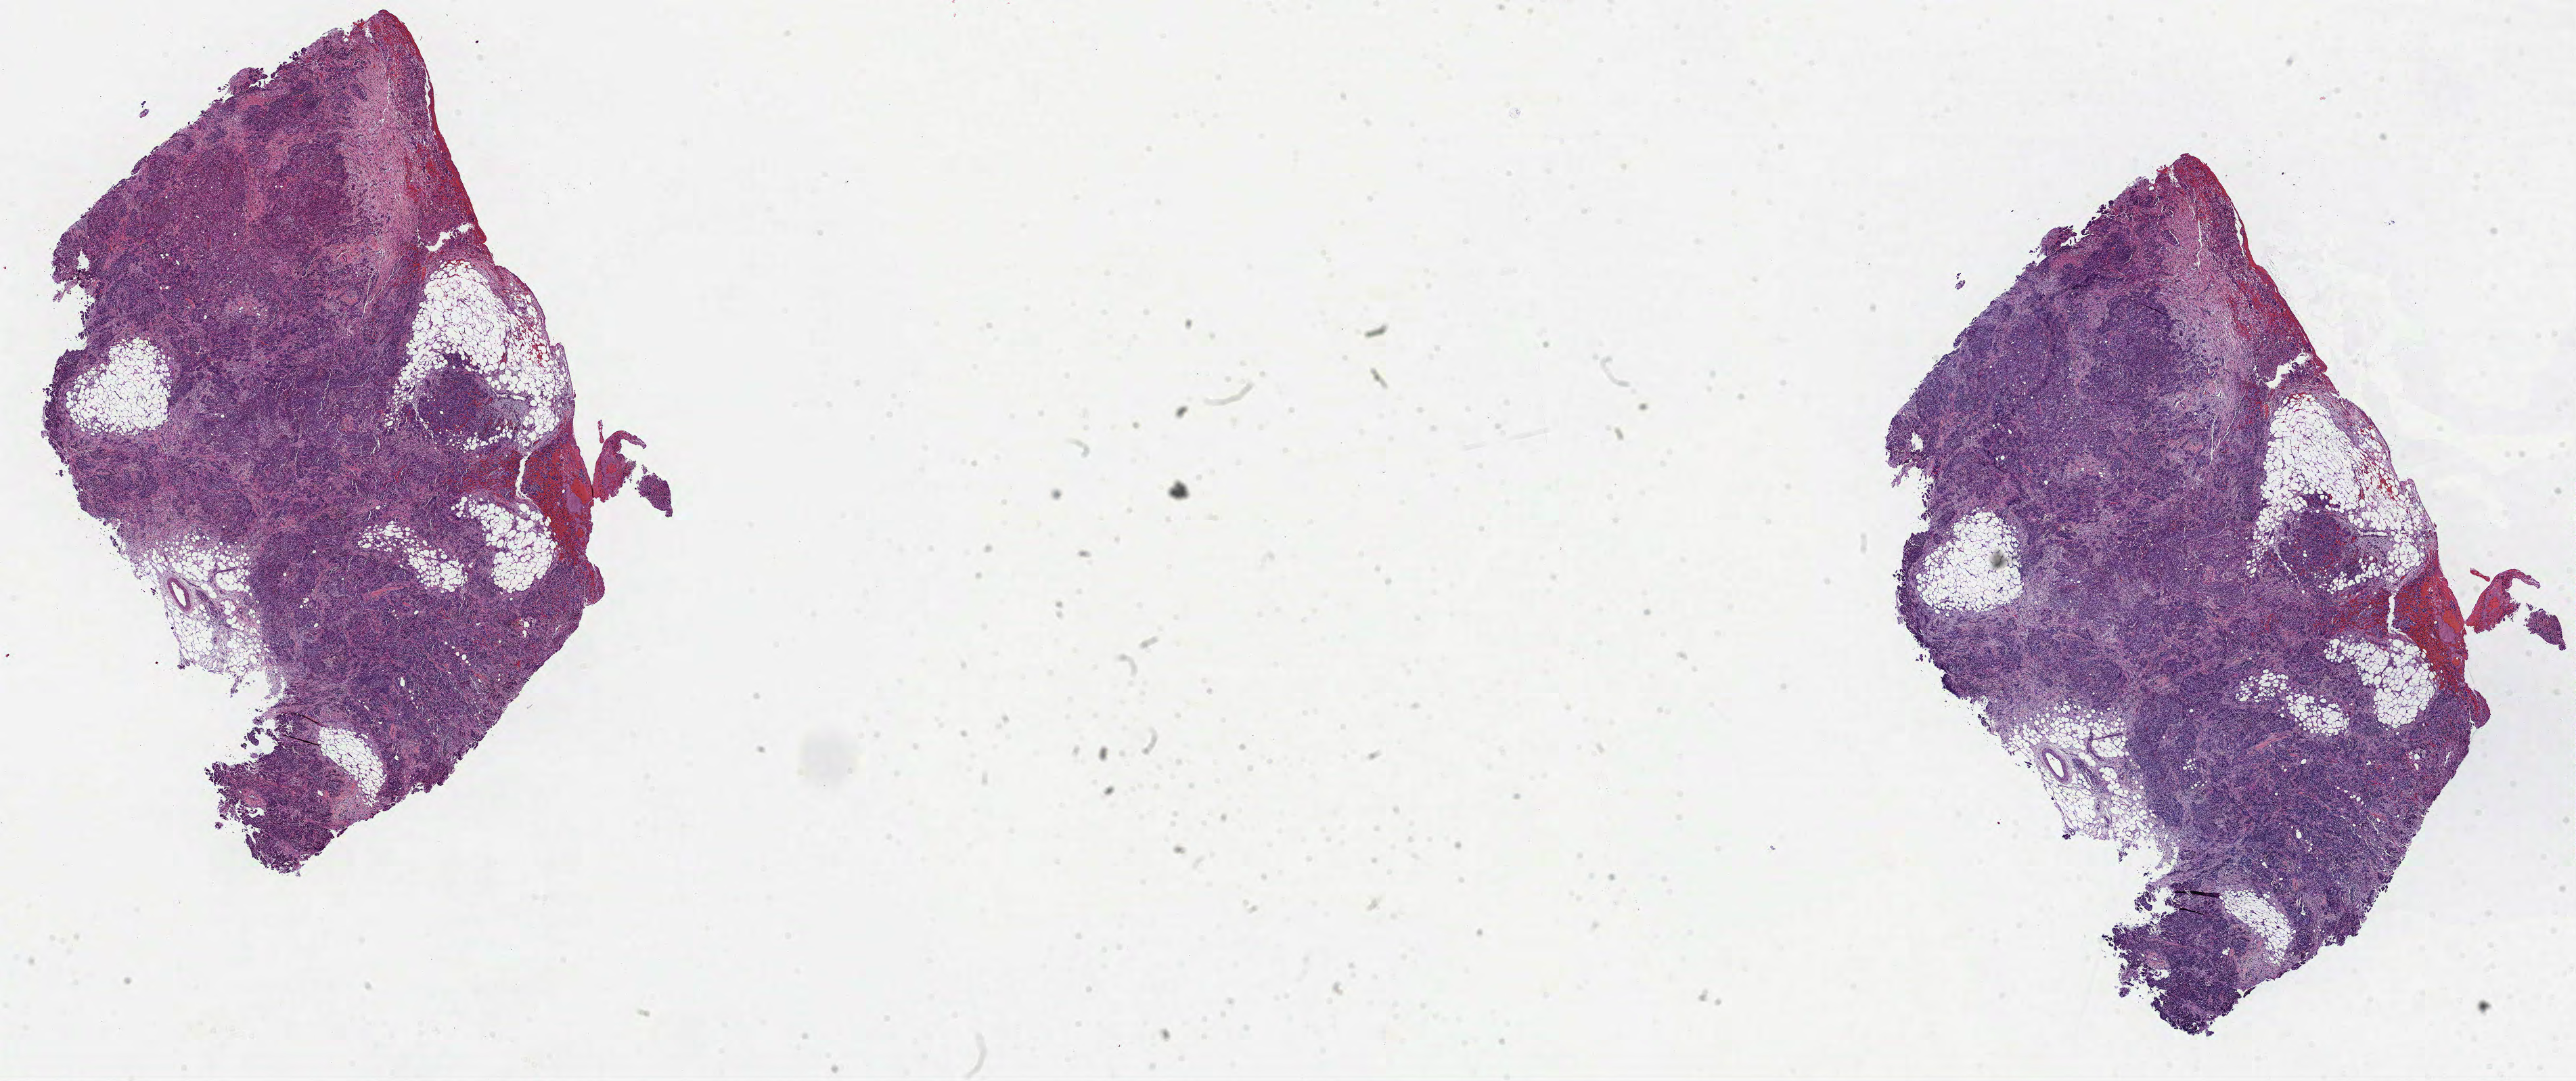
Whole-slide histology image, H&E-stained — a low-resolution overview of the entire scanned area, about 30.7 x 12.9 mm. Formalin-fixed paraffin-embedded (FFPE) diagnostic section. Ovary, primary tumour sample. Female, age 61 years at initial diagnosis. Histologic grade: G3 (poorly differentiated).
FIGO stage: IV. Laterality: bilateral. Diagnosis: Serous cystadenocarcinoma, NOS.